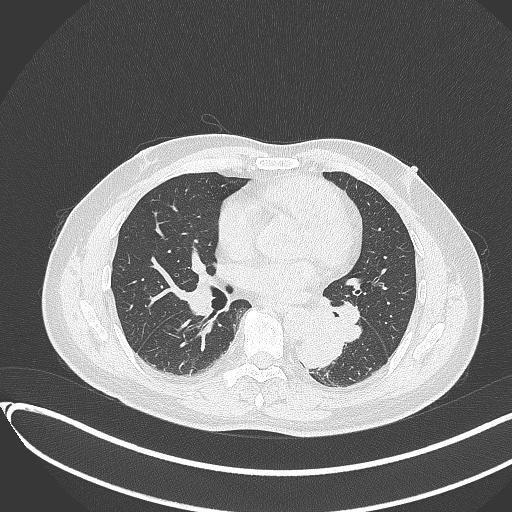
Chest CT, one axial slice; position 166 of 417 along the scan axis; reconstruction kernel B70f; lung window (W 1500 / L -600 HU); 1 mm slice thickness; 512 × 512 image matrix. Male patient, age 54 years. From the clinical record (not read from this slice): clinical TNM (as recorded): T3 N0 M0.
Annotated regions visible in this slice (bounding box drawn by a radiologist):
- lung tumour (recorded histology: squamous cell carcinoma): bounding box [x1, y1, x2, y2] px = [294, 328, 345, 373]